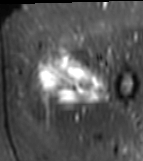
MRI of an extremity soft-tissue mass, one axial slice; STIR; MR volume resampled by the dataset authors to the PET/CT grid (not the native acquisition matrix); 3.27 mm slice thickness; 143 × 161 image matrix, field of view 140 × 157 mm. Female patient. Case-level facts recorded for this patient, not image findings: histological type: myxofibrosarcoma; grade: intermediate; site of the primary tumour: left thigh.
Annotated regions visible in this slice (expert contour drawn on MRI and transferred to this co-registered scan by the dataset authors):
- gross tumour volume including surrounding oedema: box from (x=33, y=47) to (x=109, y=111) px
- gross tumour volume (mass): (x=37, y=51)–(x=105, y=111)